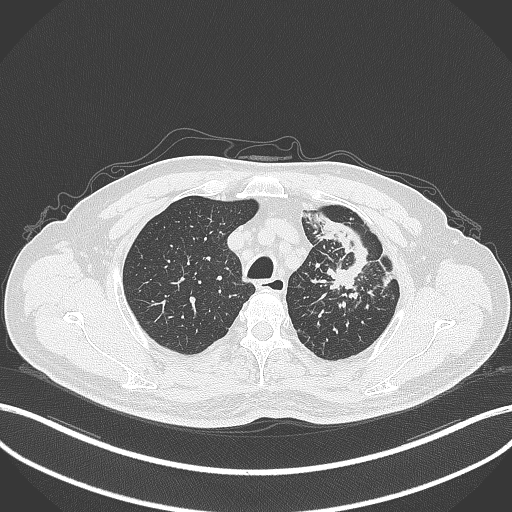
Chest CT, one axial slice. Slice 290 of 386 in the series (ordered by position). 120 kVp. Lung window (W 1500 / L -600 HU). 1 mm slice thickness. 512 × 512 image matrix, field of view 400 × 400 mm. Male patient, age 69 years. From the clinical record (not read from this slice): clinical TNM (as recorded): T2a N2 M0; histopathological grade: G2-3.
Structures marked on this image (bounding box drawn by a radiologist):
- lung tumour (recorded histology: adenocarcinoma): box from (x=307, y=206) to (x=373, y=300) px